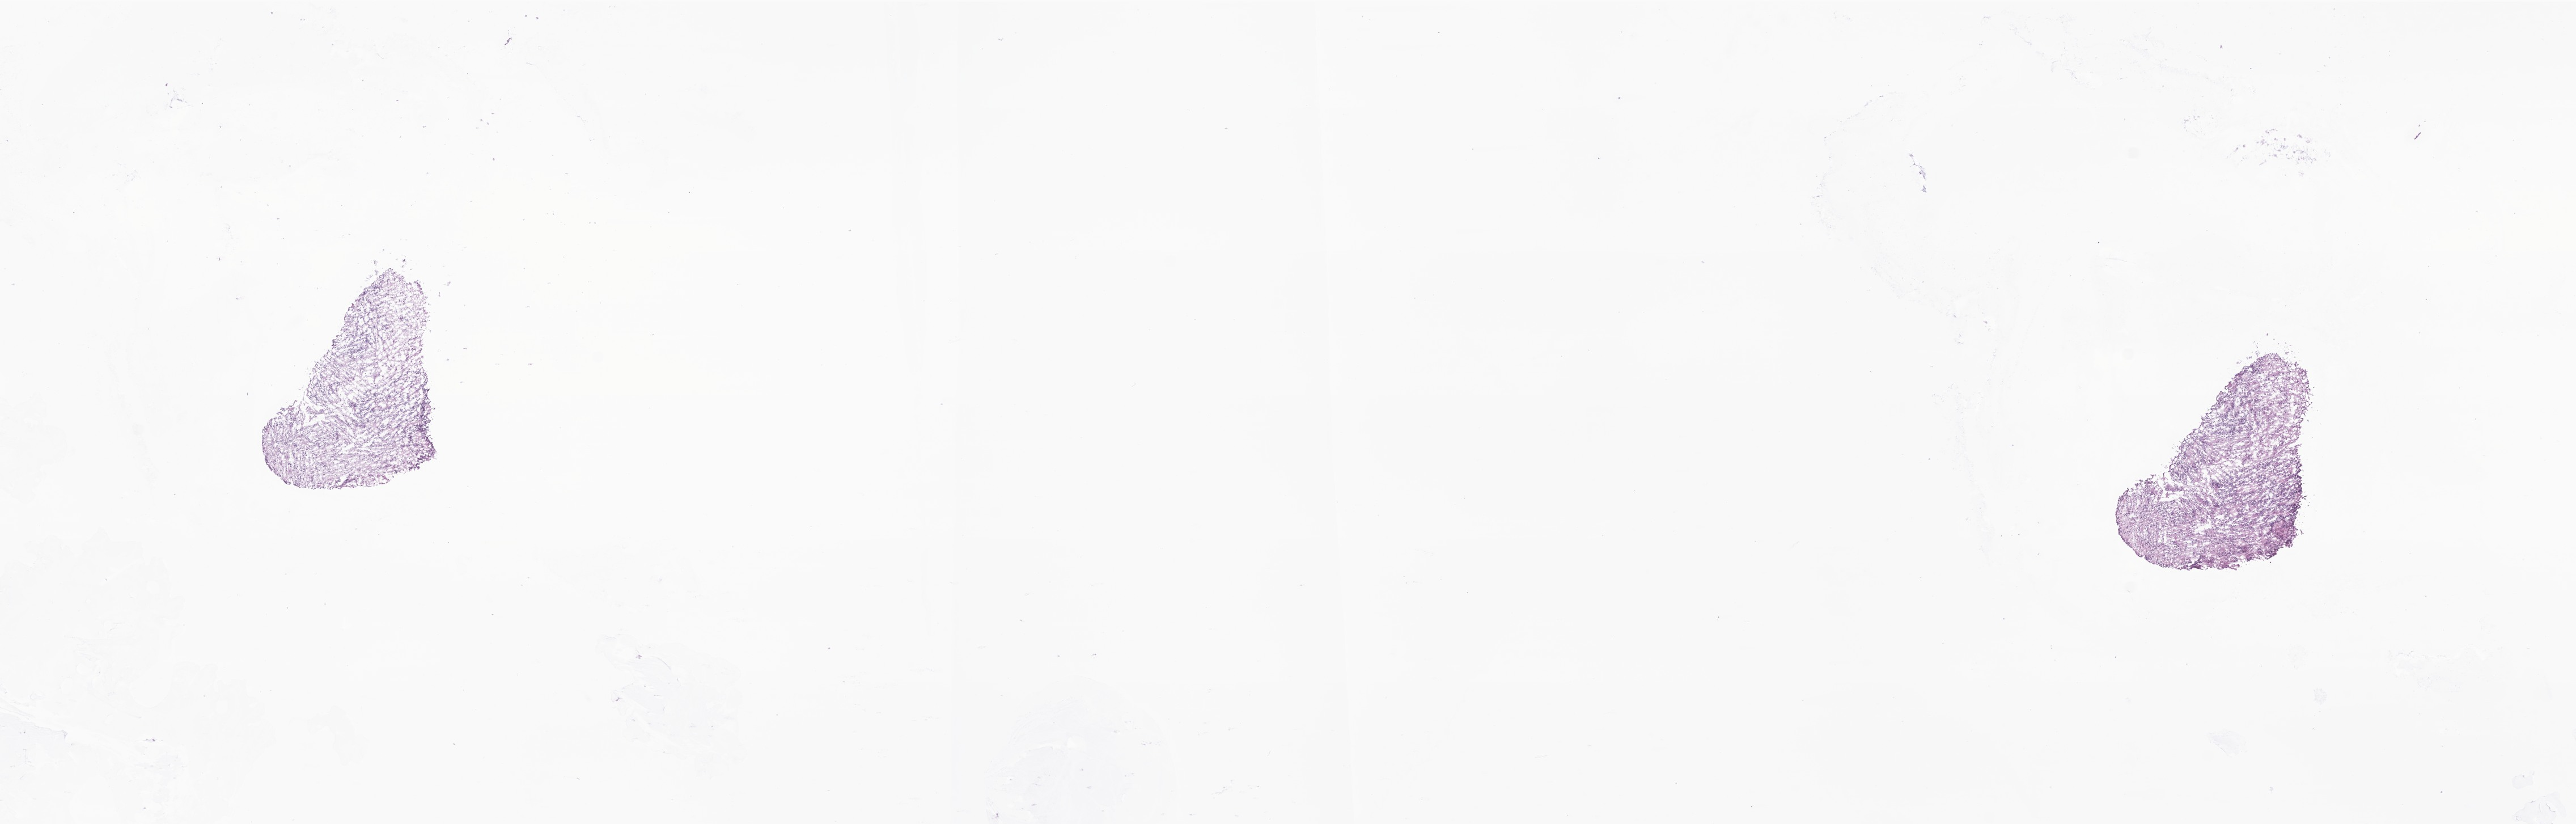
Digitized hematoxylin and eosin (H&E)-stained section of tumor tissue from the brain stem — low-resolution overview of the scanned area, about 19.2 x 6.1 mm. Frozen section (OCT-embedded). Patient: female, age 716 days.
Diagnosis: Ependymoma, NOS.